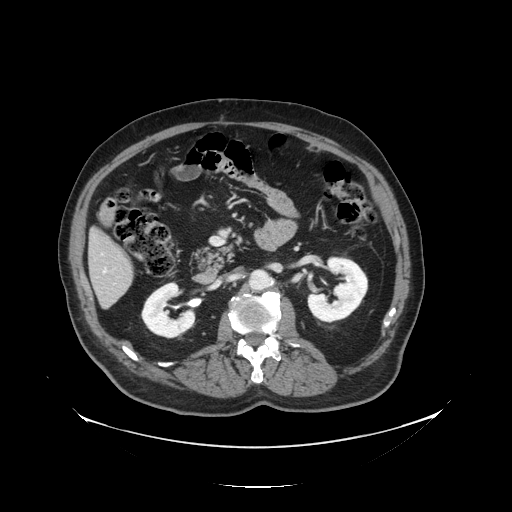
Contrast-enhanced abdominal CT, one axial slice. Position 50 of 138 along the scan axis. Reconstruction kernel STANDARD. 120 kVp. Intravenous contrast given. Soft-tissue window (W 400 / L 40 HU). 512 × 512 image matrix. Male patient, age 77 years. From the clinical record (not read from this slice): diagnosis: colorectal cancer liver metastases, imaged before liver resection; multiple liver metastases: no; largest metastasis: 1.5 cm; disease in both lobes: no.
Structures marked on this image (expert manual segmentation):
- liver: bounding box [x1, y1, x2, y2] px = [90, 234, 135, 308]
- planned liver remnant (the part of the liver to remain after resection): [90, 234, 133, 280]